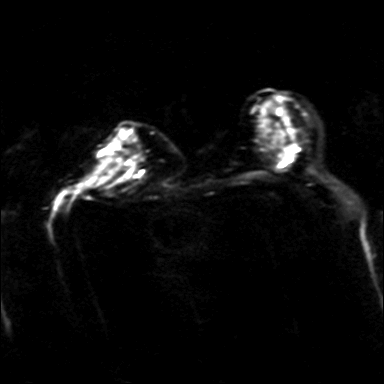
Breast MRI, one axial slice; position 22 of 40 along the scan axis; diffusion-weighted series; image 2 of 4 stored at this slice position (different b-values; order by instance number); 3 T; 4 mm slice thickness; 384 × 384 image matrix. Female patient.
Annotated regions visible in this slice (manually delineated by an expert):
- tumour on diffusion-weighted imaging: bounding box <101,145,120,155> (left, top, right, bottom; pixels)